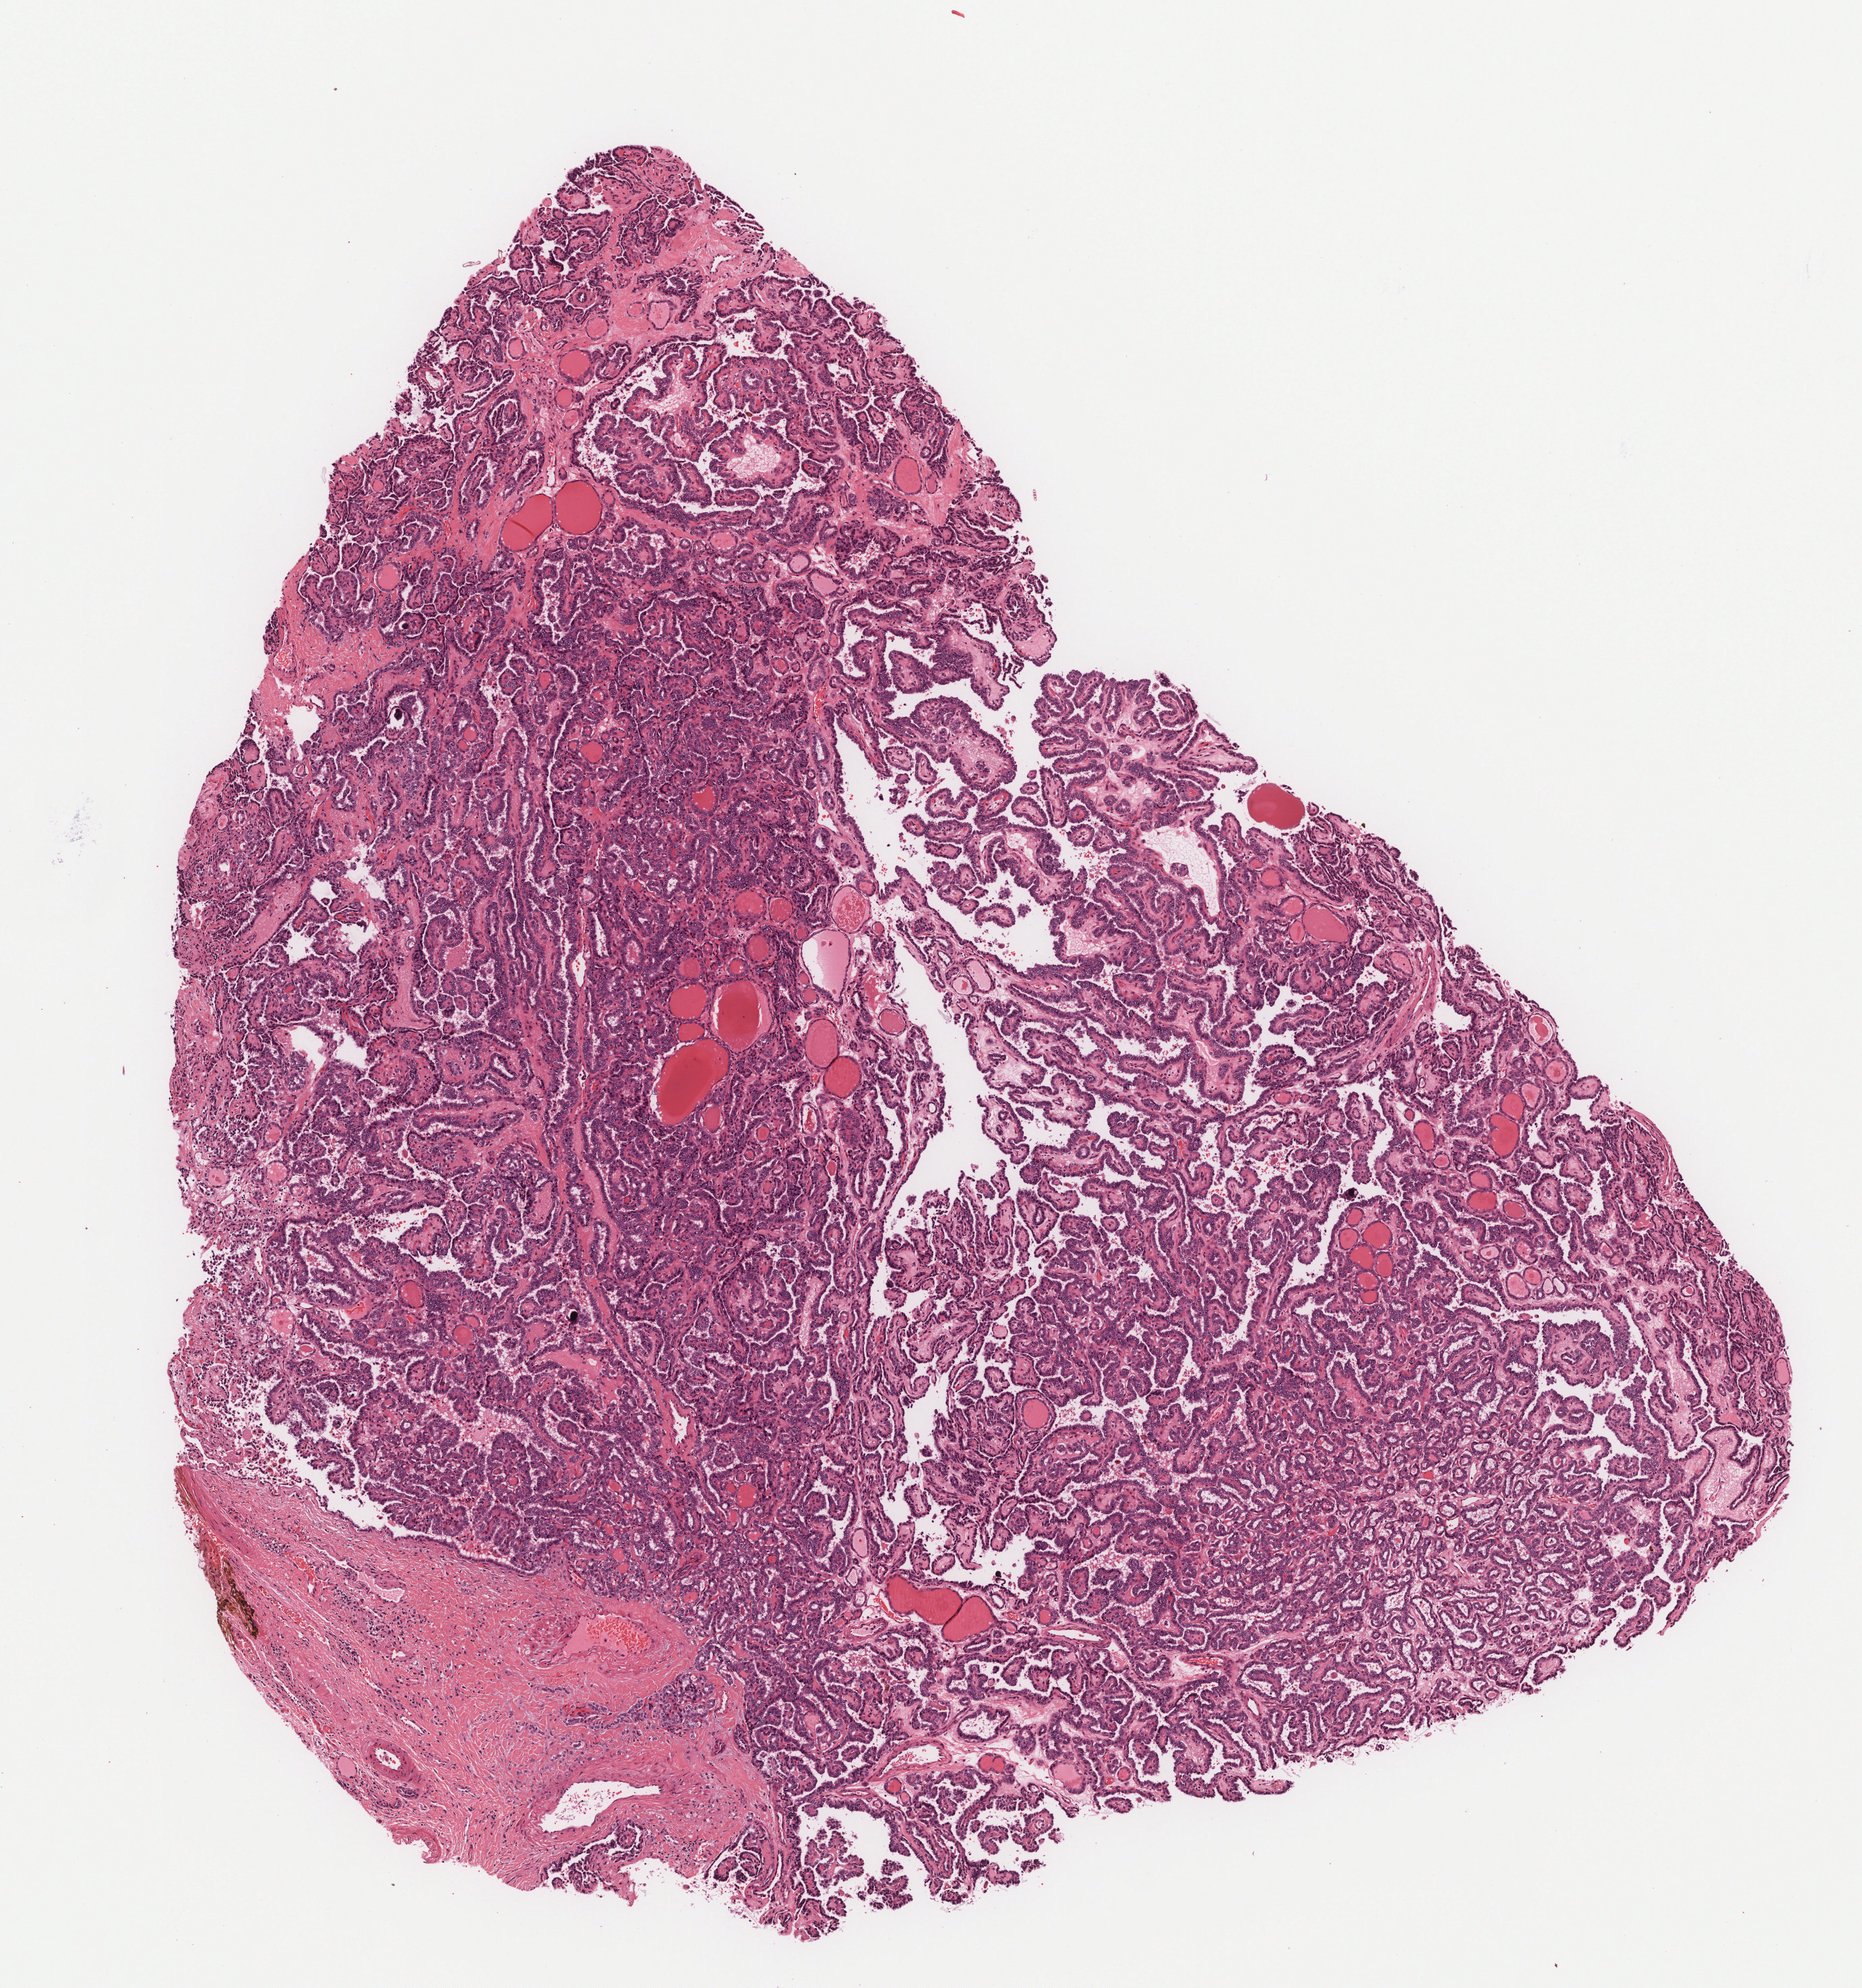
Digitized H&E tissue section (whole slide) — whole scanned area (about 5.6 x 5.9 mm) shown as a low-resolution overview. Formalin-fixed paraffin-embedded (FFPE) diagnostic section. Sample: primary tumour, thyroid. Female patient; age at initial diagnosis 85 years.
Diagnosis: Papillary adenocarcinoma, NOS.